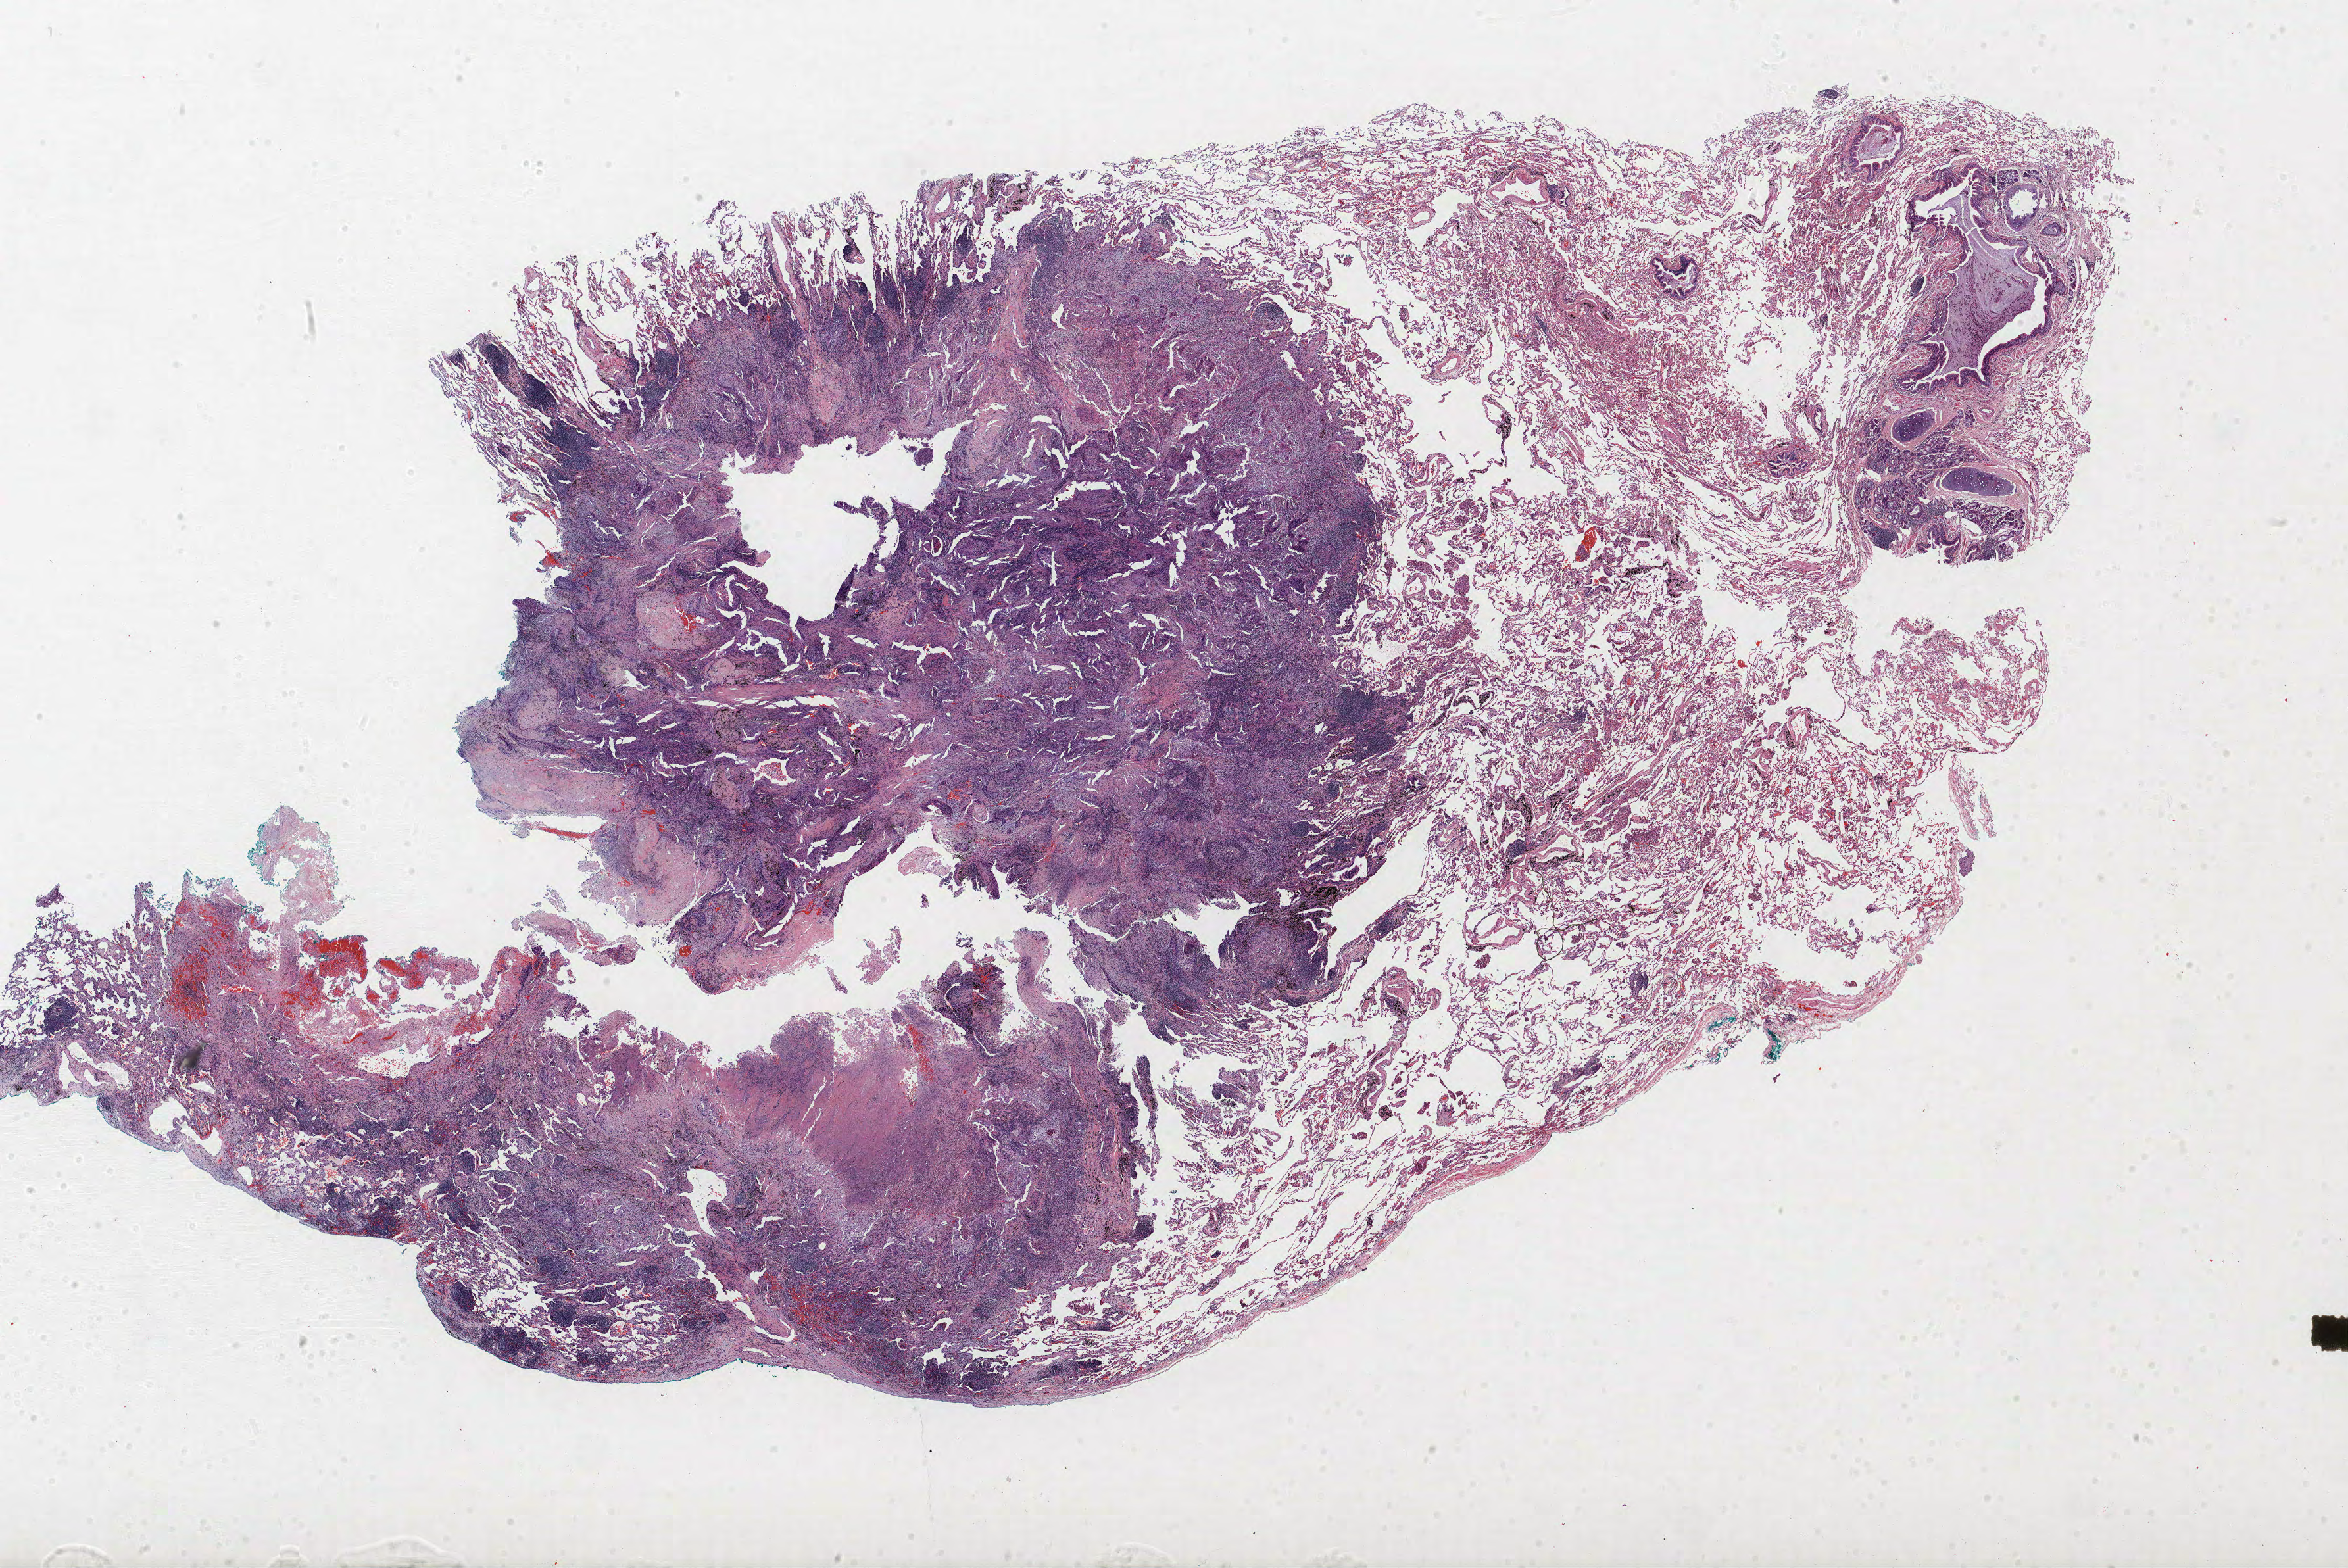
H&E-stained whole-slide image — shown as a low-resolution overview of the whole scanned area (about 28.6 x 19.1 mm, from a 40x scan). Formalin-fixed paraffin-embedded (FFPE) section. Lung tissue. Male, age 69 at enrolment. Current smoker at enrolment. Grade: poorly differentiated (G3).
Participant's lung-cancer diagnosis: Squamous cell carcinoma, NOS (ICD-O-3 8070/3). Stage (AJCC 6th edition): IA. Tumour size (pathology): 15 mm. Primary tumour location (clinical record): right middle lobe.